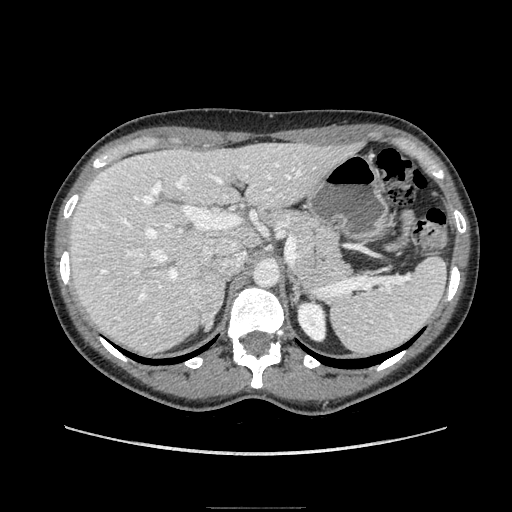
Contrast-enhanced abdominal CT, one axial slice; position 121 of 193 along the scan axis; soft-tissue window (W 400 / L 40 HU); 512 × 512 image matrix, field of view 380 × 380 mm. Female patient. Case-level facts recorded for this patient, not image findings: diagnosis: adrenocortical carcinoma; tumour side: right adrenal; tumour size at pathology: 3 cm; Ki-67 index: 4 %; stage (as recorded): 1.
Annotated regions visible in this slice (semi-automatically segmented with operator editing):
- mass: bounding box <195,271,224,329> (left, top, right, bottom; pixels)